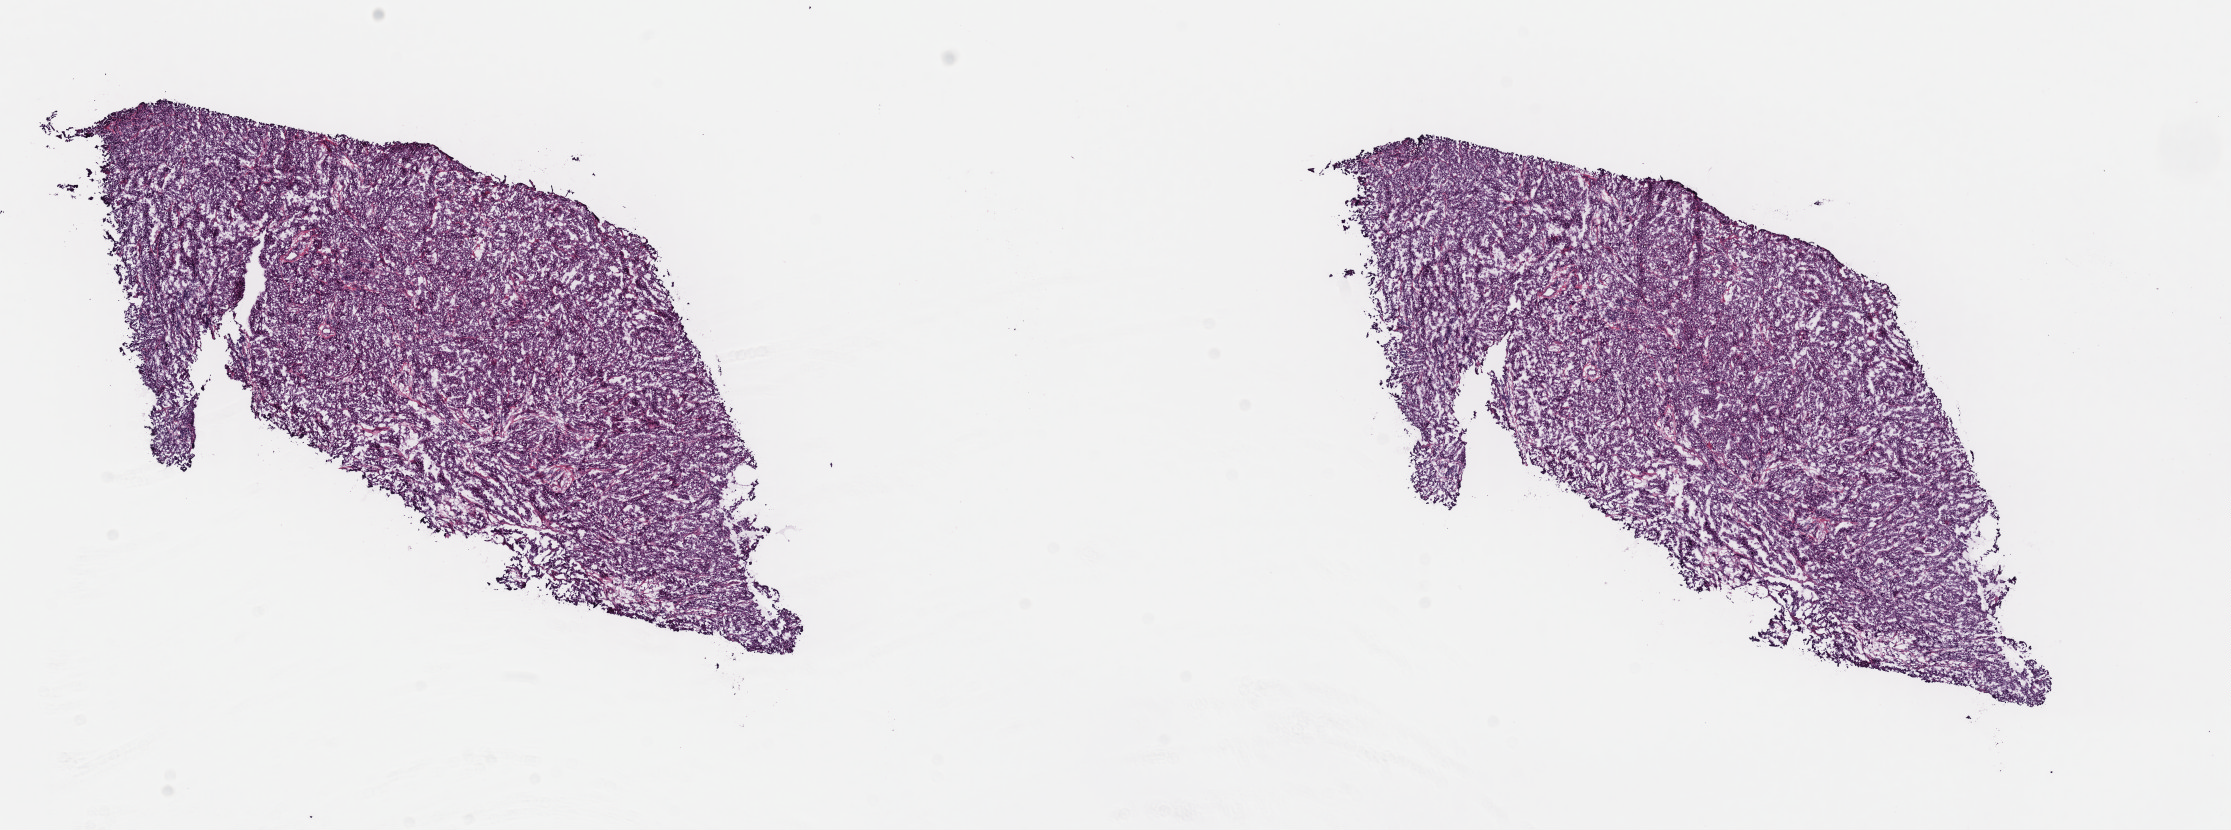
Whole-slide histology image, Hematoxylin and eosin (H&E) stained — a low-resolution overview of the entire scanned area, about 17.6 x 6.5 mm (slide scanned at 40x). Frozen section from the top of the tissue portion. Metastatic tumour sample, sampled site not recorded. Male patient; age at initial diagnosis 55 years. Composition of this section per pathologist review: tumour cells 85%, tumour nuclei 85%, normal cells 0%, stromal cells 14%, necrosis 1%. Inflammatory infiltration, as recorded: lymphocyte infiltration 3%, monocyte infiltration 1%, neutrophil infiltration 0%.
This section: metastatic tumour tissue. Patient diagnosis: Malignant melanoma, NOS.